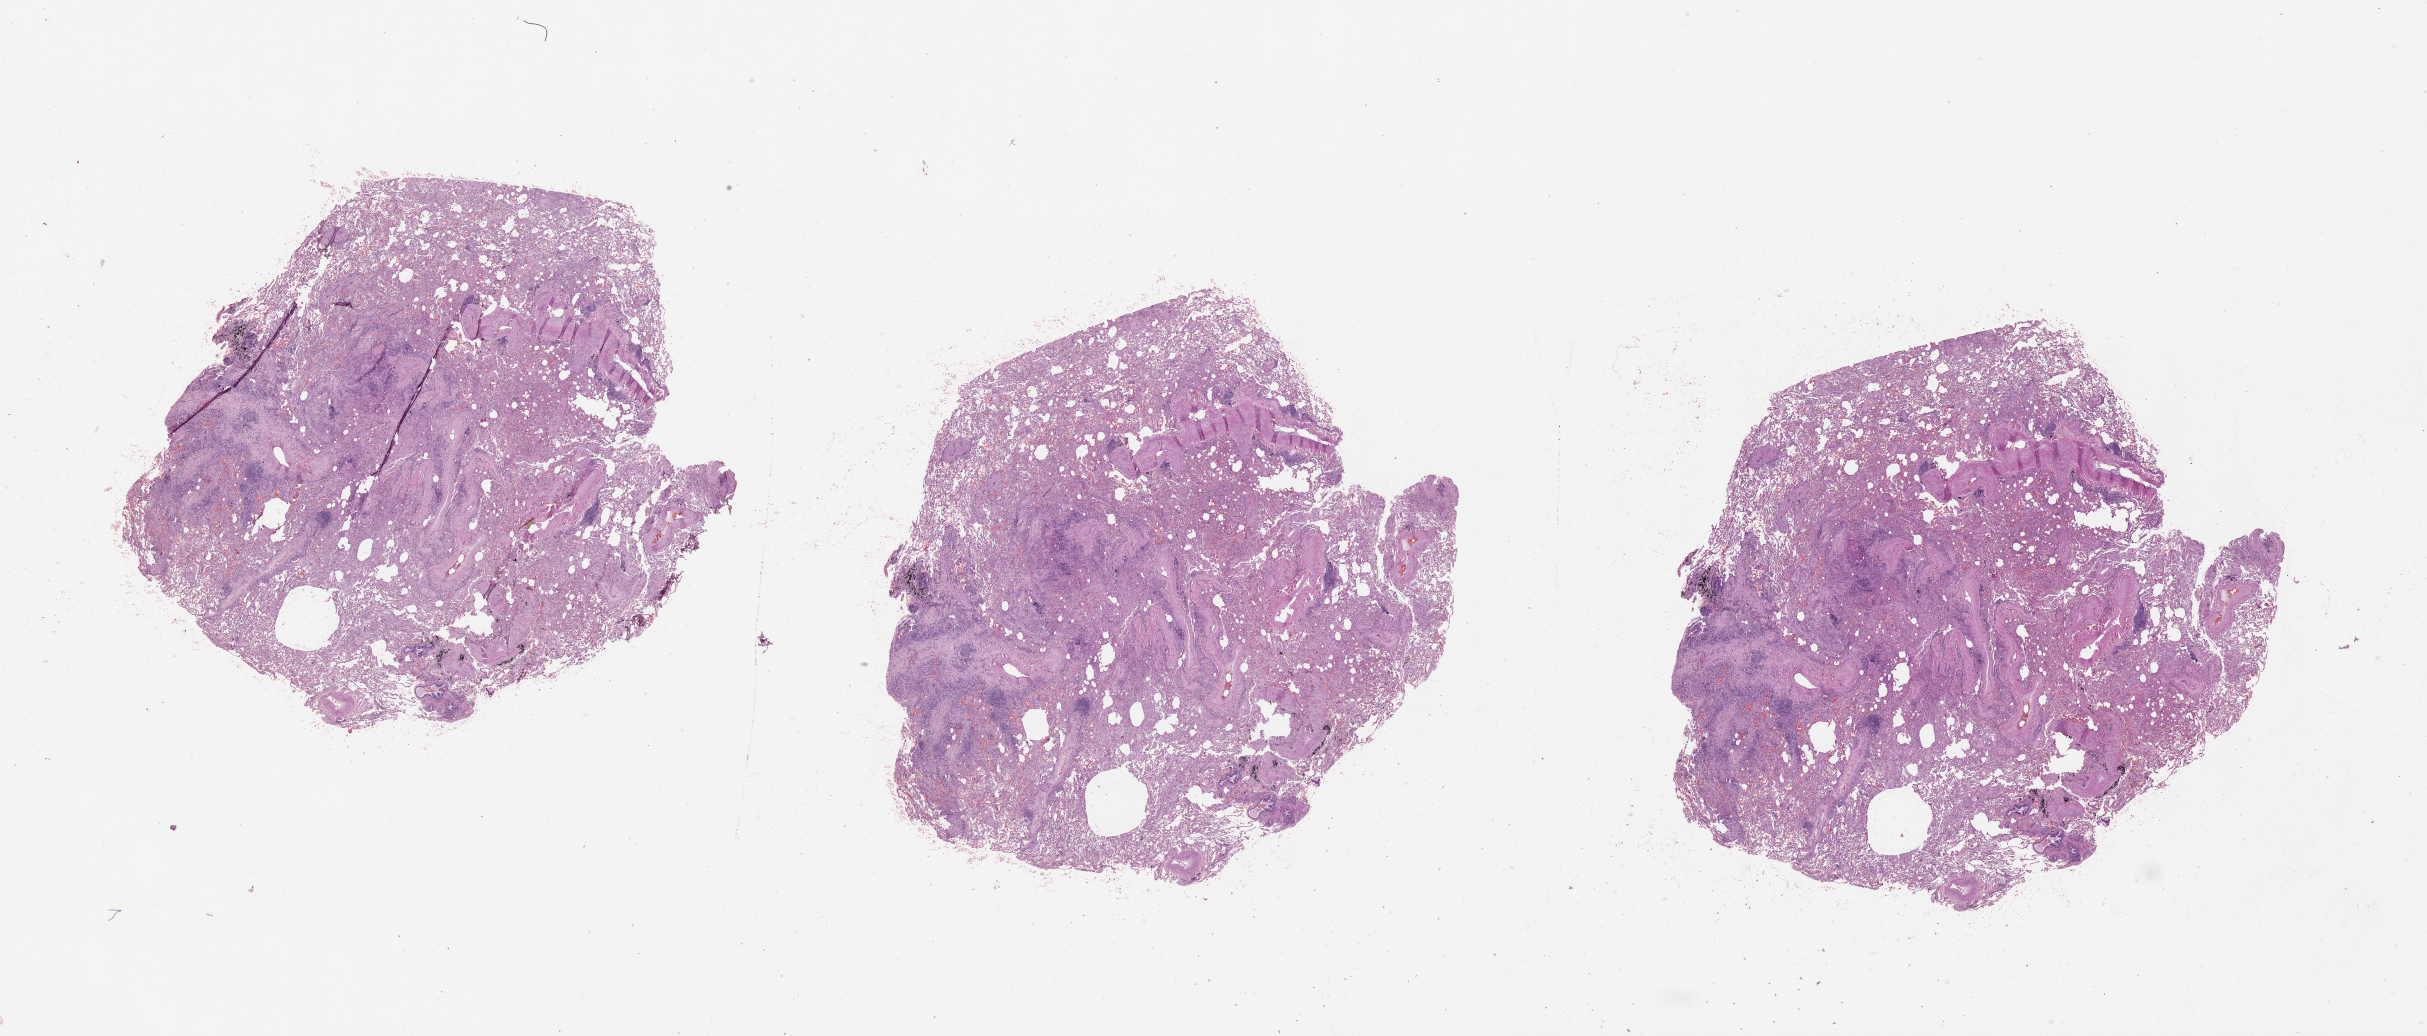
Digitized H&E-stained tissue section (whole slide), low-resolution overview of the scanned area, about 39.1 x 16.7 mm (from a 20x scan), lung, normal (non-tumour) tissue. 74-year-old male patient.
This section: normal (non-tumour) tissue from the same patient. Patient diagnosis (cohort enrolment): squamous cell carcinoma (lung).